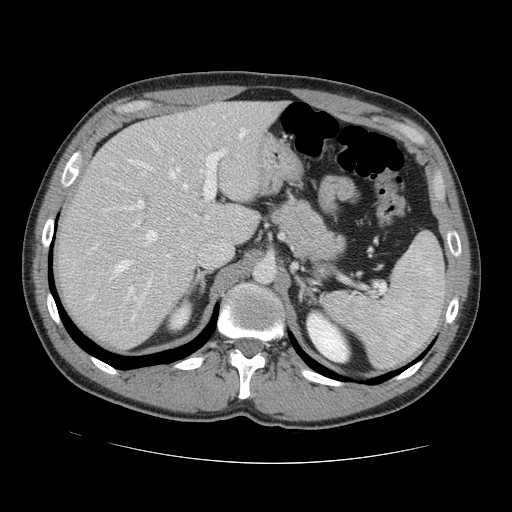
Contrast-enhanced abdominal CT, one axial slice. Position 91 of 131 along the scan axis. 120 kVp. Intravenous contrast given. Soft-tissue window (W 400 / L 40 HU). 2.5 mm slice thickness. 512 × 512 image matrix. Male patient, age 40 years. Case-level facts recorded for this patient, not image findings: diagnosis: colorectal cancer liver metastases, imaged before liver resection.
Outlined on this slice (manually delineated by an expert):
- hepatic veins: bounding box <90,135,243,319> (left, top, right, bottom; pixels)
- liver: <59,101,281,348>
- planned liver remnant (the part of the liver to remain after resection): <100,102,282,244>
- portal vein (with intrahepatic branches): <91,149,226,314>